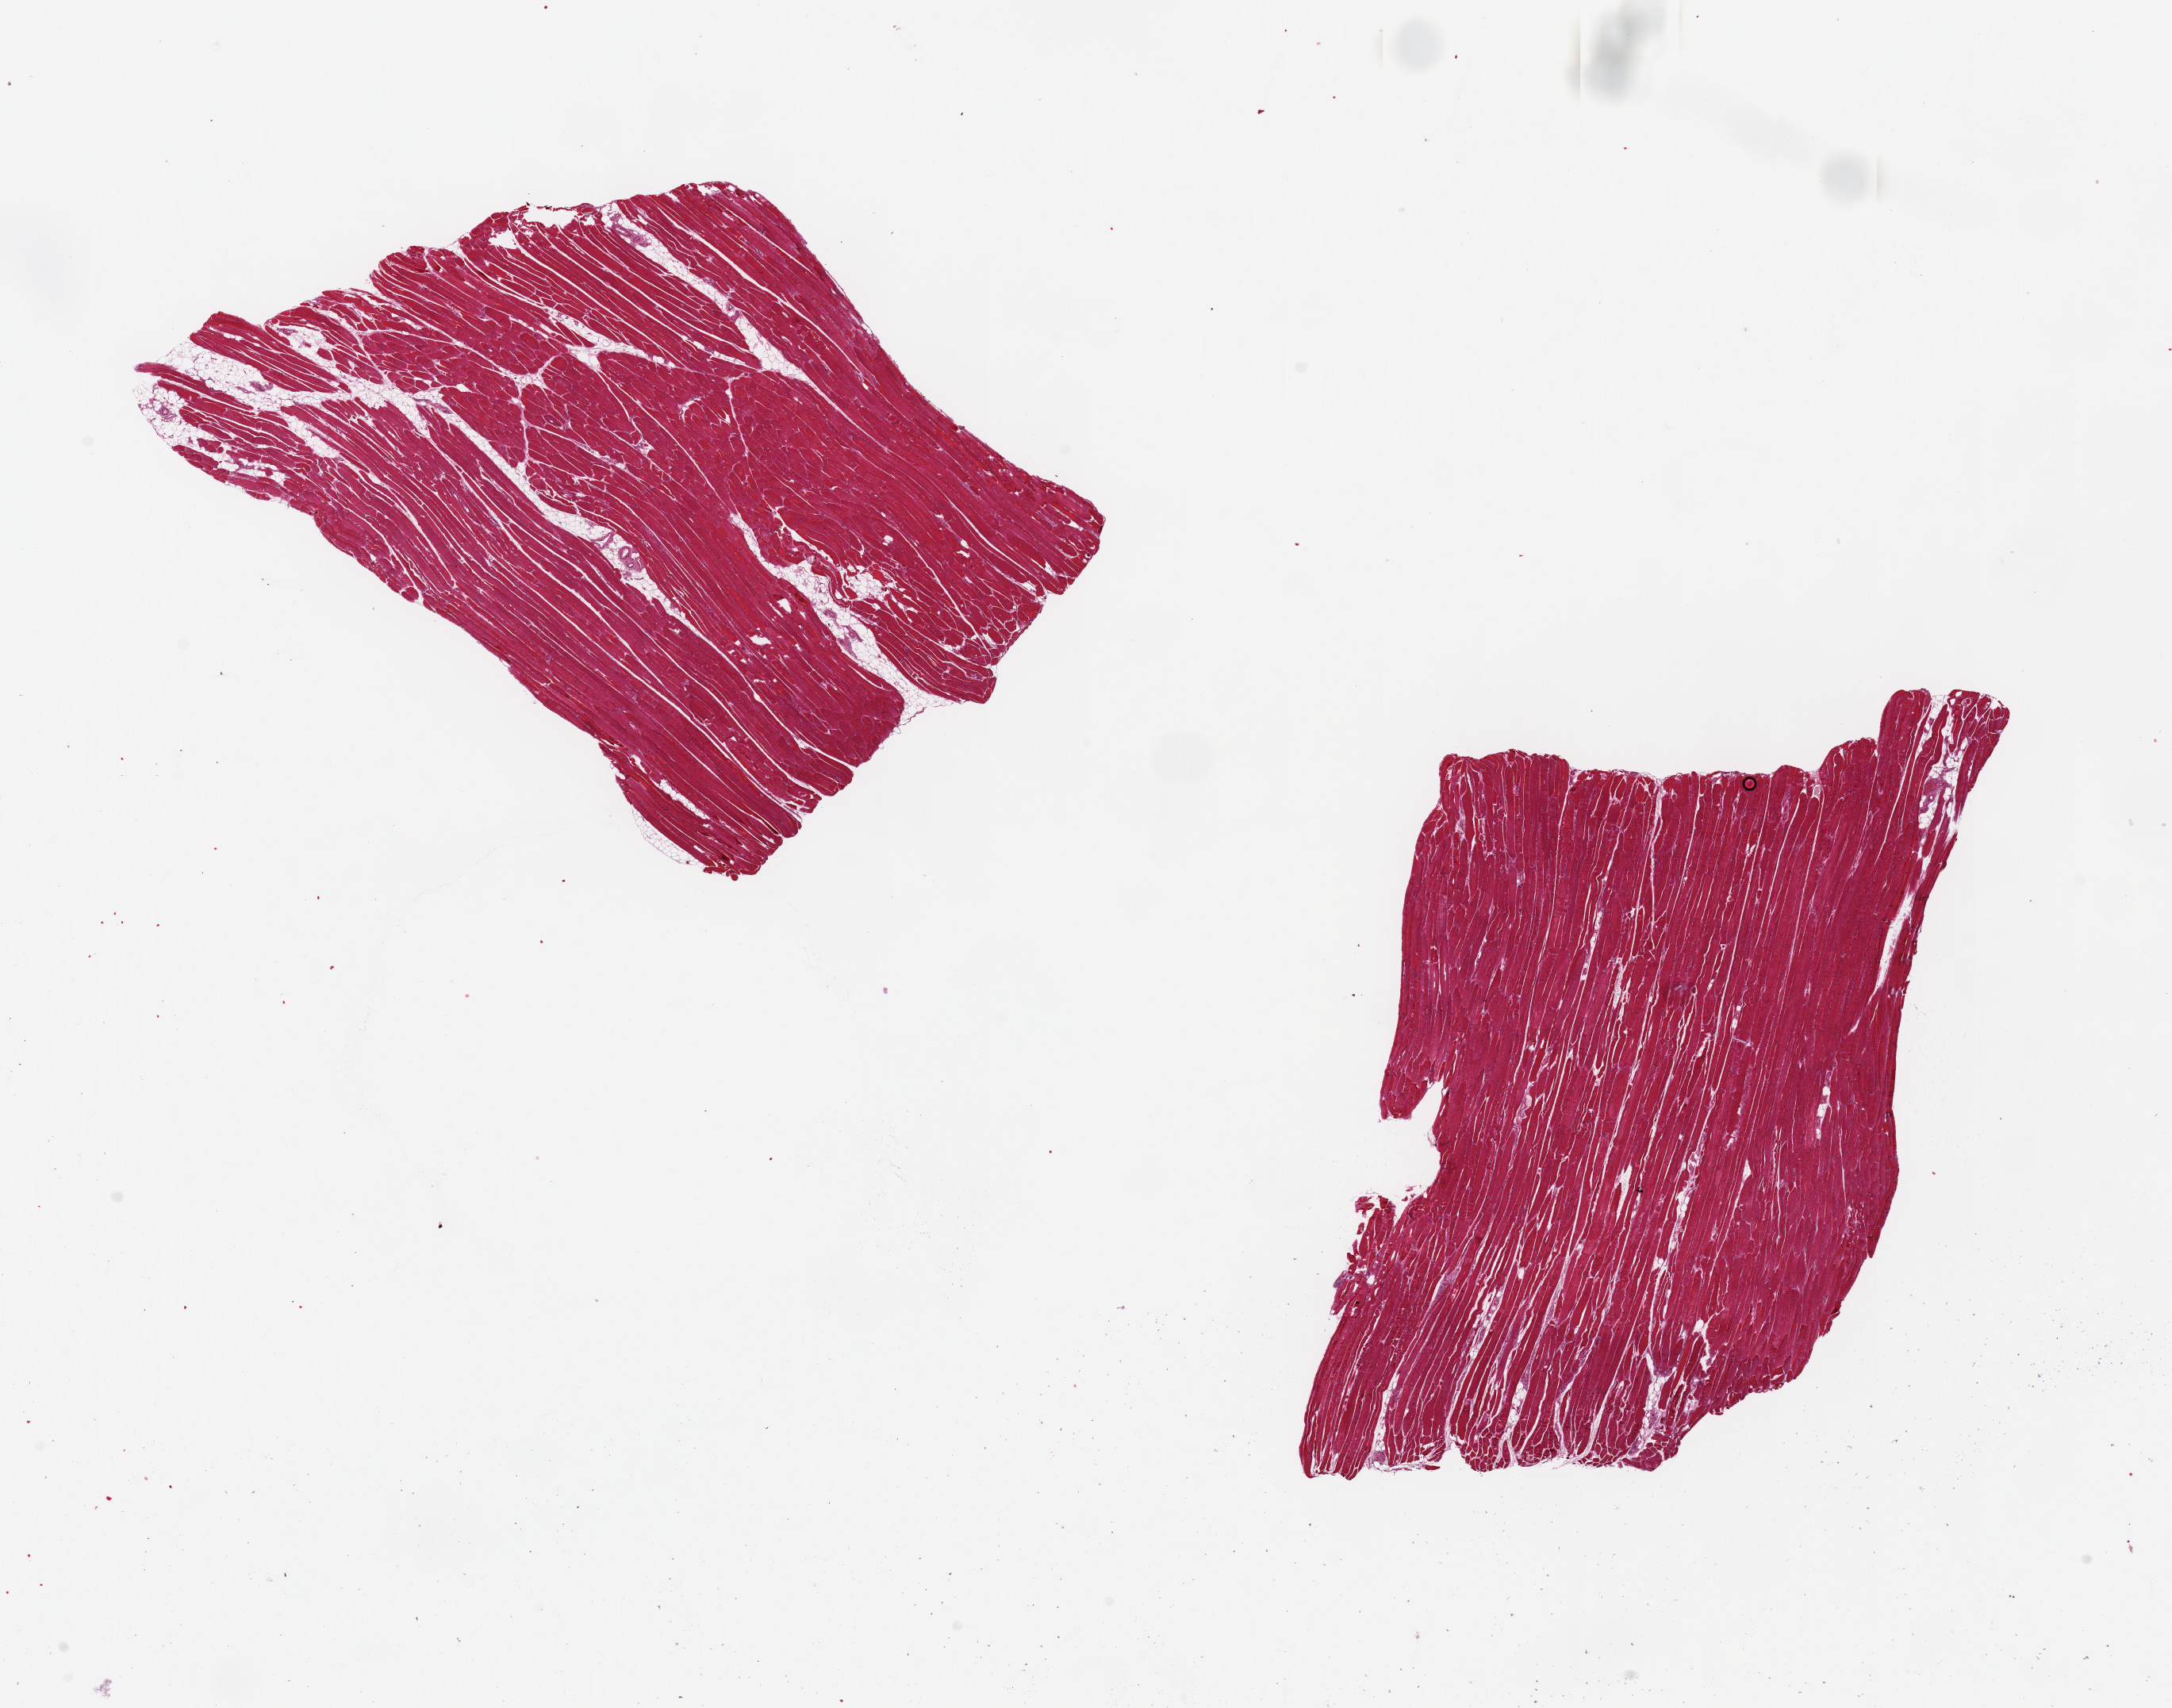
Hematoxylin and eosin (H&E) whole-slide image, low-resolution overview of the scanned area, about 21.7 x 17.0 mm, PAXgene-fixed, paraffin-embedded tissue, target tissue: skeletal muscle, tissue donor sample. Donor: female.
• pathologist's review note for this sample: 2 pieces, 7x5 & 8x5mm